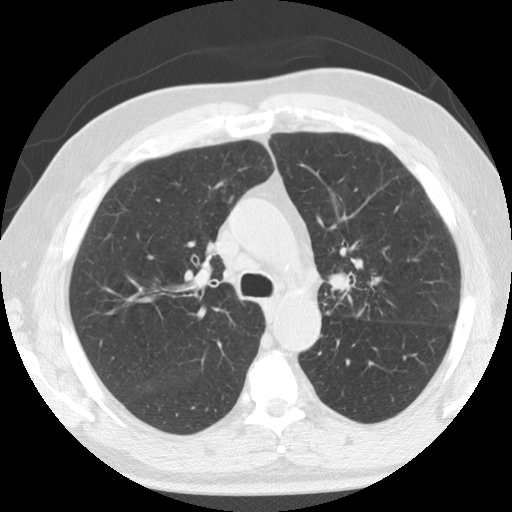
Low-dose screening chest CT, one axial slice. Slice 90 of 133 in the series (ordered by position). Reconstruction kernel STANDARD. Lung window (W 1500 / L -600 HU). 2.5 mm slice thickness. 512 × 512 image matrix.
Structures marked on this image (outlined manually by an expert reader):
- lesion 1 (tumor, upper lobe of left lung): bounding box [x1, y1, x2, y2] px = [330, 272, 351, 292]